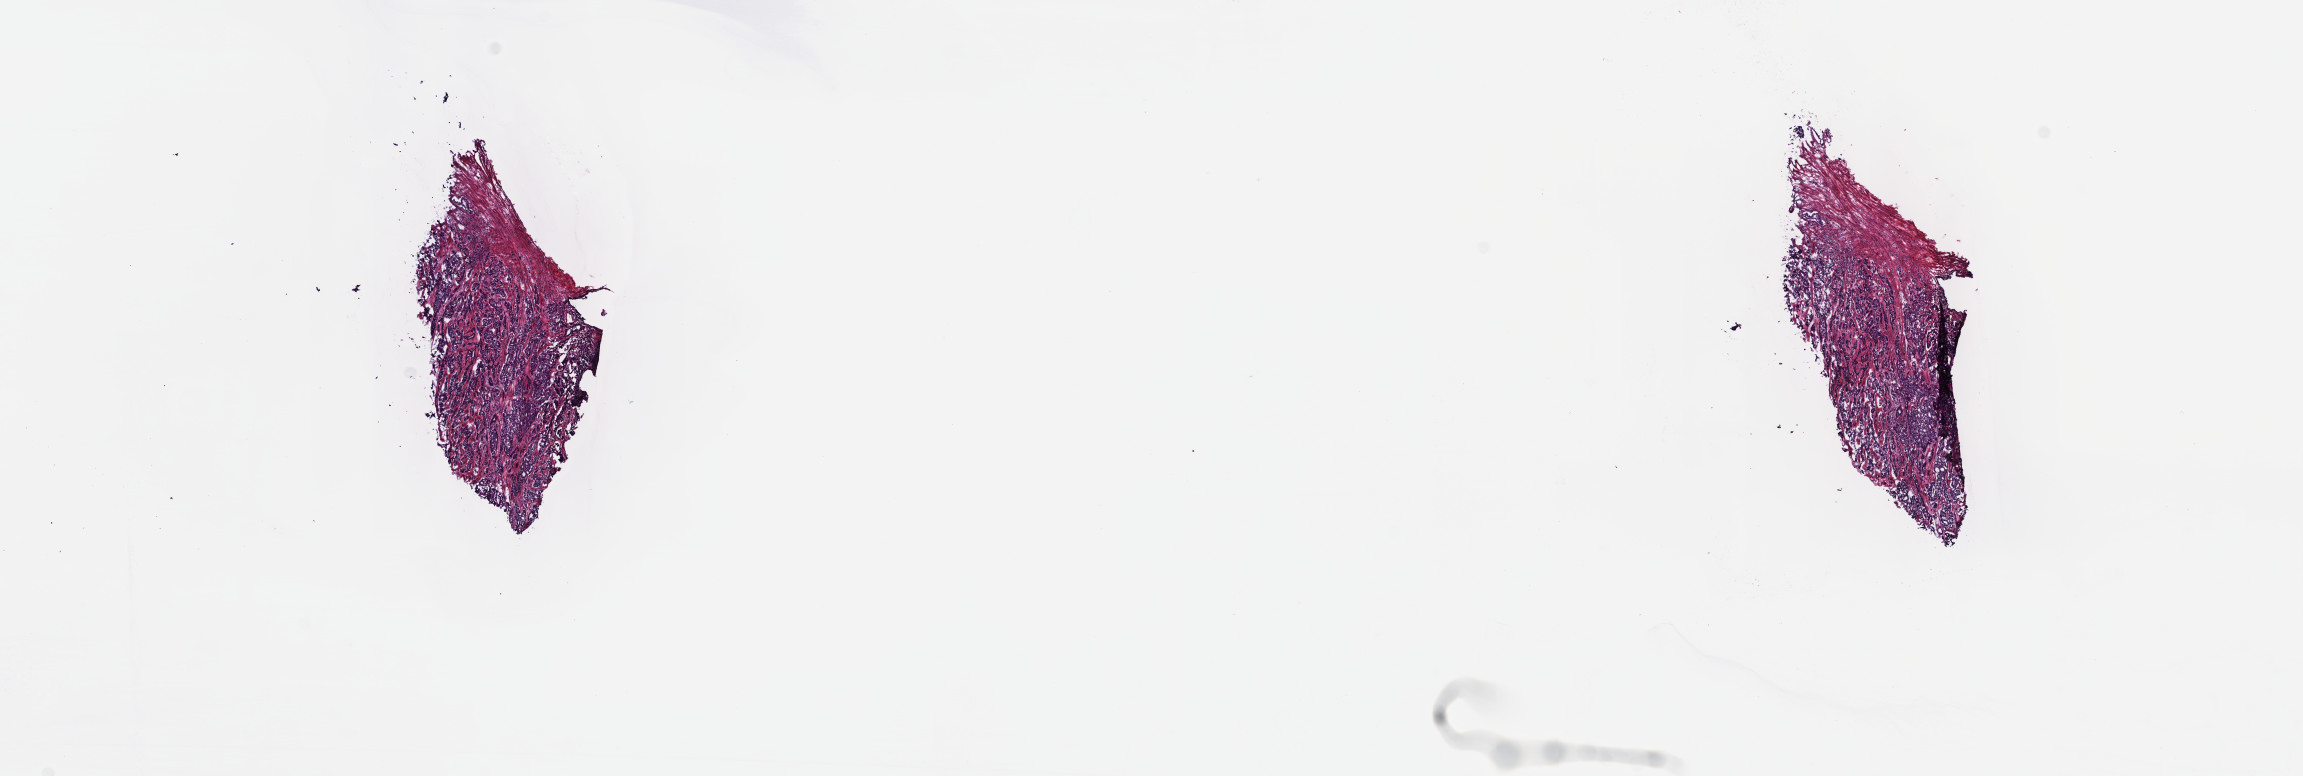
Whole-slide histology image, H&E-stained — low-resolution overview of the scanned area, about 18.6 x 6.3 mm (from a 40x scan); frozen section from the top of the tissue portion; prostate, primary tumour sample. Male, age 63 years at initial diagnosis. Gleason score: 9 (5+4). Composition of this section per pathologist review: tumour cells 70%, tumour nuclei 70%, normal cells 0%, stromal cells 30%, necrosis 0%. Infiltration values recorded for this section: lymphocyte infiltration 40%, monocyte infiltration 20%, neutrophil infiltration 20%.
Laterality: bilateral. Histologic diagnosis: Adenocarcinoma, NOS (prostate gland). Lymph nodes positive (case pathology): 1 of 3 examined.